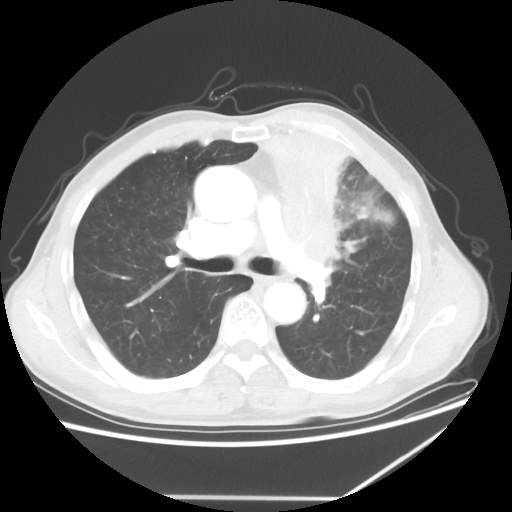
Chest CT, one axial slice; position 39 of 64 along the scan axis; 100 kVp; lung window (W 1500 / L -600 HU); 512 × 512 image matrix. Male patient, age 64 years. Case-level facts recorded for this patient, not image findings: clinical TNM (as recorded): T1c N1 M1; histopathological grade: G2.
Outlined on this slice (rectangle marked by the reading radiologist):
- lung tumour (recorded histology: squamous cell carcinoma): bounding box (x1, y1, x2, y2) in pixels: (267, 119, 361, 286)